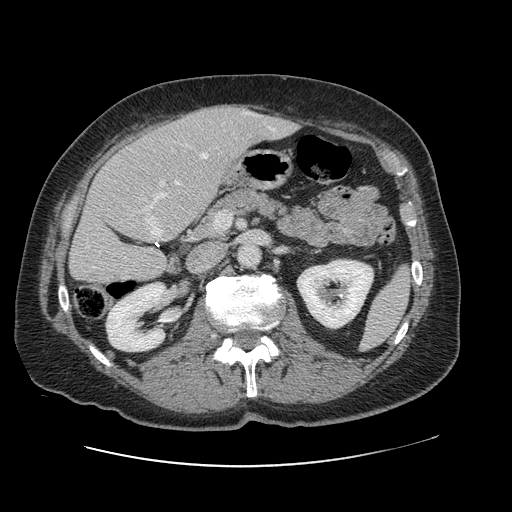
Contrast-enhanced abdominal CT, one axial slice. Slice 45 of 138 in the series (ordered by position). Intravenous contrast given. Soft-tissue window (W 400 / L 40 HU). 2.5 mm slice thickness. 512 × 512 image matrix, field of view 402 × 402 mm. Male patient, age 71 years. From the clinical record (not read from this slice): diagnosis: colorectal cancer liver metastases, imaged before liver resection; multiple liver metastases: no; largest metastasis: 3.3 cm; chemotherapy before resection: no.
Structures marked on this image (manually delineated by an expert):
- hepatic veins: bounding box [x1, y1, x2, y2] px = [93, 128, 274, 269]
- liver: [70, 106, 296, 284]
- planned liver remnant (the part of the liver to remain after resection): [70, 137, 196, 285]
- portal vein (with intrahepatic branches): [160, 181, 164, 185]